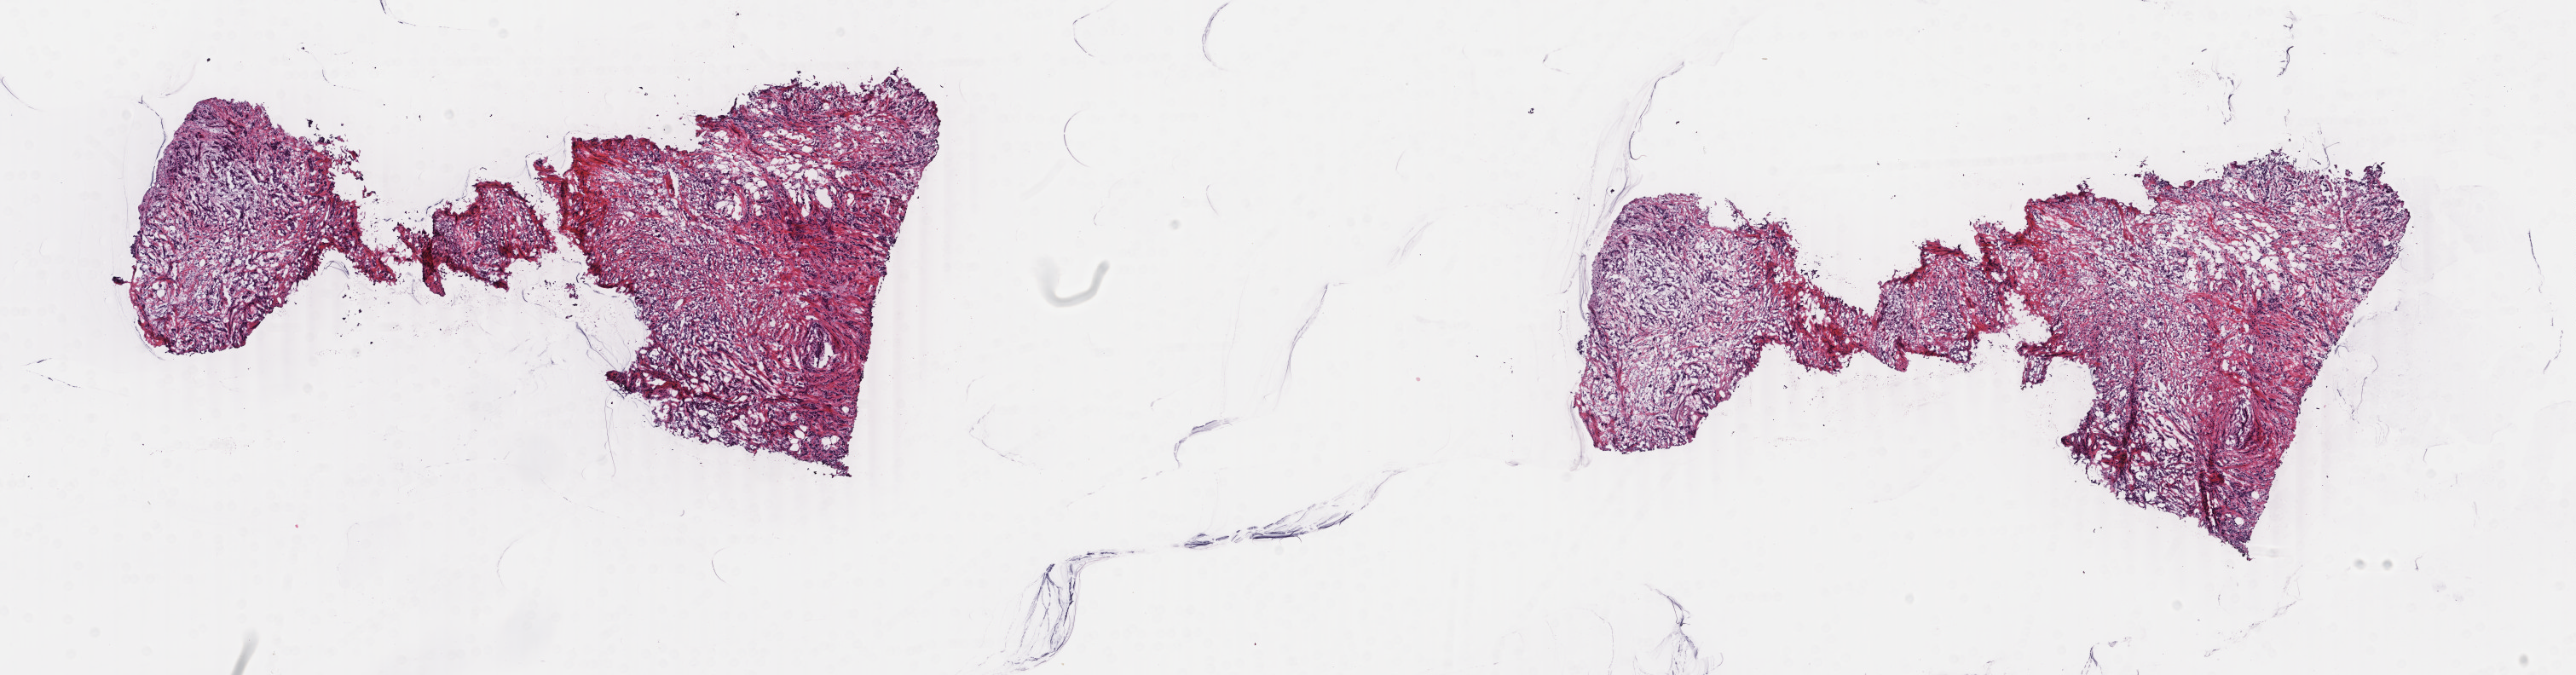
Whole-slide histology image, H&E-stained, whole scanned area (about 24.0 x 6.3 mm) shown as a low-resolution overview. Frozen section from the bottom of the tissue portion. Primary tumour sample from the breast. Patient: female, age at initial diagnosis 44 years. Slide review estimates, as recorded: tumour cells 100%, tumour nuclei 60%, normal cells 0%, stromal cells 0%, necrosis 0%. Infiltration values recorded for this section: lymphocyte infiltration 0%, monocyte infiltration 0%, neutrophil infiltration 0%.
Laterality: right. Histologic diagnosis: Infiltrating duct carcinoma, NOS. AJCC pathologic stage: IIIA. Lymph nodes positive (case pathology): 3 of 11 examined.